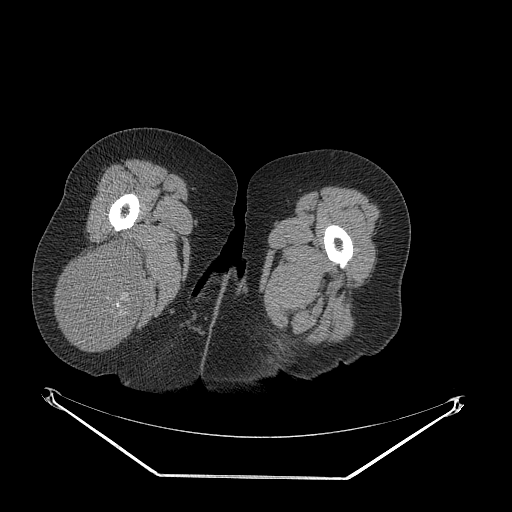
CT of an extremity soft-tissue mass (from a PET/CT study), one axial slice. Position 41 of 257 along the scan axis. 140 kVp. Soft-tissue window (W 400 / L 40 HU). 3.75 mm slice thickness. 512 × 512 image matrix, field of view 500 × 500 mm. Female patient. From the clinical record (not read from this slice): histological type: synovial sarcoma; grade: intermediate; site of the primary tumour: right buttock.
Structures marked on this image (expert contour drawn on MRI and transferred to this co-registered scan by the dataset authors):
- gross tumour volume including surrounding oedema: box from (x=62, y=246) to (x=145, y=344) px
- gross tumour volume (mass): (x=62, y=246)–(x=145, y=344)